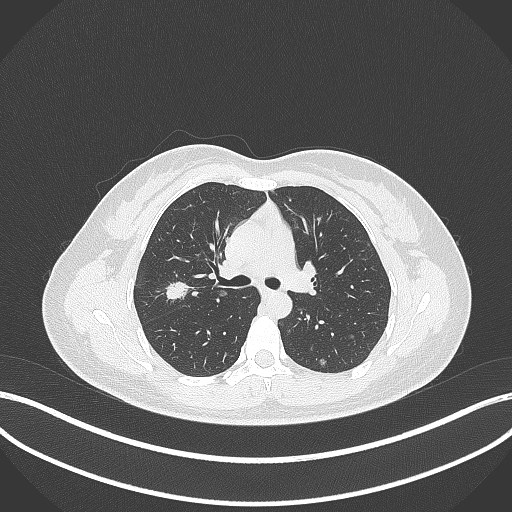
Chest CT, one axial slice; slice 215 of 307 in the series (ordered by position); lung window (W 1500 / L -600 HU); 1 mm slice thickness; 512 × 512 image matrix, field of view 400 × 400 mm. Female patient, age 33 years. From the clinical record (not read from this slice): clinical TNM (as recorded): T1c N0 M0.
Annotated regions visible in this slice (bounding box drawn by a radiologist):
- lung tumour (recorded histology: adenocarcinoma): bounding box [x1, y1, x2, y2] px = [162, 279, 192, 303]